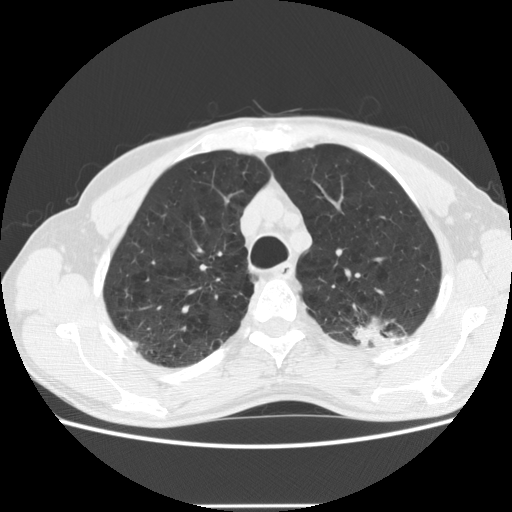
Low-dose screening chest CT, one axial slice. Reconstruction kernel STANDARD. Lung window (W 1500 / L -600 HU). 2.5 mm slice thickness. 512 × 512 image matrix, field of view 352 × 352 mm.
Structures marked on this image (outlined manually by an expert reader):
- lesion 1 (tumor, upper lobe of left lung): box from (x=354, y=318) to (x=396, y=347) px